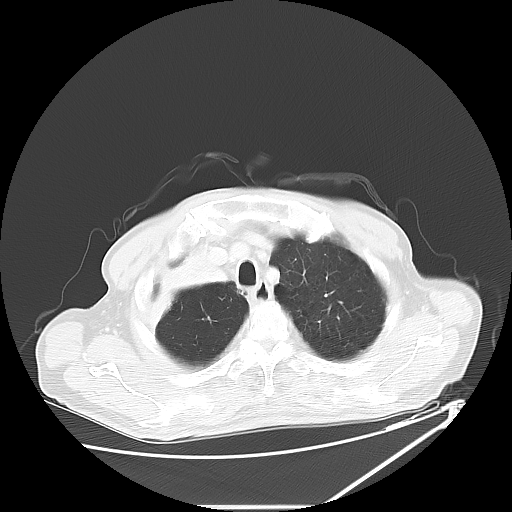
Chest CT, one axial slice; slice 52 of 60 in the series (ordered by position); reconstruction kernel LUNG; lung window (W 1500 / L -600 HU); 512 × 512 image matrix, field of view 410 × 410 mm. Male patient, age 73 years. Case-level facts recorded for this patient, not image findings: clinical TNM (as recorded): T2a N1 M0.
Outlined on this slice (bounding box drawn by a radiologist):
- lung tumour (recorded histology: squamous cell carcinoma): bounding box (x1, y1, x2, y2) in pixels: (137, 248, 231, 327)